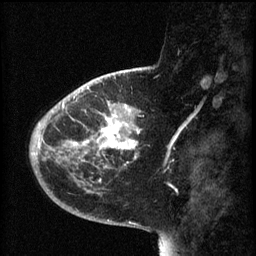
Breast MRI (dynamic contrast-enhanced), one sagittal slice; position 19 of 60 along the scan axis; 3 images stored at this slice position (order not interpretable as contrast timing); 1.5 T; TE 4.2 ms, TR 8.1 ms; 2 mm slice thickness; 256 × 256 image matrix, field of view 200 × 200 mm. Female patient, age 44 years.
Structures marked on this image (semi-automatically segmented with operator editing):
- analysis volume of interest (the breast-tissue region the enhancement analysis was run in; not a lesion): bounding box <59,110,141,169> (left, top, right, bottom; pixels)
- tumour enhancement mask (voxels above the 70 % enhancement threshold inside the analysis volume of interest): <73,112,141,157>